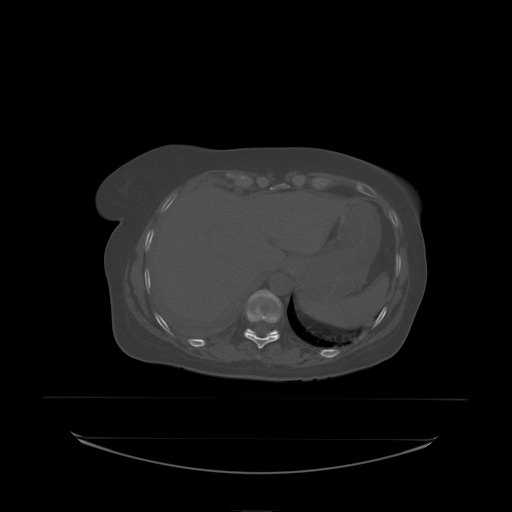
CT including the spine, one axial slice. Slice 111 of 242 in the series (ordered by position). Bone window (W 1800 / L 400 HU). 2.5 mm slice thickness. 512 × 512 image matrix, field of view 500 × 500 mm. Female patient, age 53 years. Case-level facts recorded for this patient, not image findings: primary cancer: lung.
Structures marked on this image (semi-automatic segmentation, software-assisted and operator-edited):
- T10 vertebra: bounding box (x1, y1, x2, y2) in pixels: (244, 307, 280, 338)
- T11 vertebra: (246, 290, 281, 336)